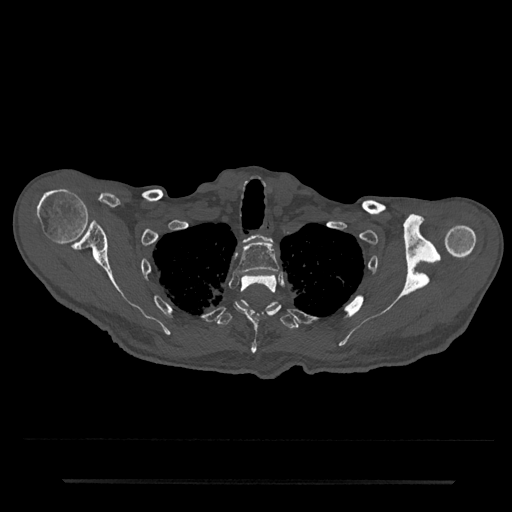
CT including the spine, one axial slice; slice 658 of 797 in the series (ordered by position); bone window (W 1800 / L 400 HU); 0.5 mm slice thickness; 512 × 512 image matrix, field of view 427 × 427 mm. Patient: male, 74 years. Case-level facts recorded for this patient, not image findings: primary cancer: prostate.
Outlined on this slice (semi-automatic segmentation, software-assisted and operator-edited):
- T1 vertebra: bounding box (x1, y1, x2, y2) in pixels: (256, 235, 273, 243)
- T2 vertebra: (236, 242, 279, 274)
- T3 vertebra: (234, 275, 281, 354)
- T4 vertebra: (216, 300, 299, 329)